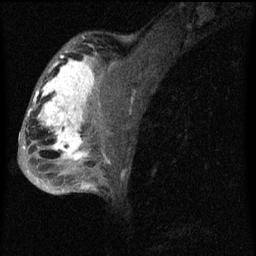
Breast MRI (dynamic contrast-enhanced), one sagittal slice. Position 40 of 60 along the scan axis. Dynamic contrast-enhanced series, image 2 of 4 at this slice position (ordered by acquisition). 1.5 T. TE 4.2 ms, TR 8 ms. 2 mm slice thickness. 256 × 256 image matrix. Patient: female, 50 years.
Annotated regions visible in this slice (semi-automatic segmentation, software-assisted and operator-edited):
- analysis volume of interest (the breast-tissue region the enhancement analysis was run in; not a lesion): bounding box <26,44,124,177> (left, top, right, bottom; pixels)
- tumour enhancement mask (voxels above the 70 % enhancement threshold inside the analysis volume of interest): <28,50,108,163>